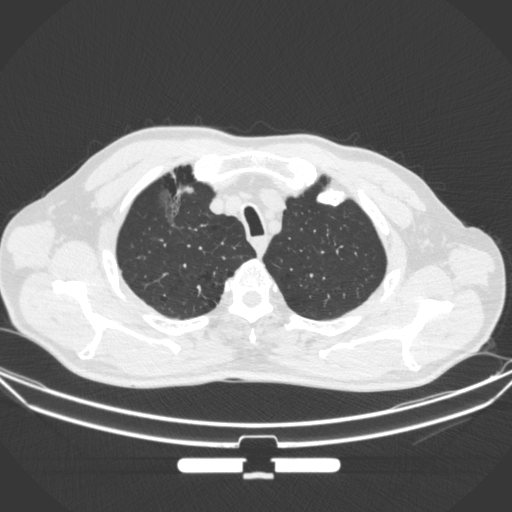
Chest CT, one axial slice; position 294 of 355 along the scan axis; 120 kVp; lung window (W 1500 / L -600 HU); 512 × 512 image matrix. Patient: male, 67 years. From the clinical record (not read from this slice): clinical TNM (as recorded): T1c N0 M0.
Annotated regions visible in this slice (rectangle marked by the reading radiologist):
- lung tumour (recorded histology: adenocarcinoma): box from (x=145, y=178) to (x=192, y=230) px